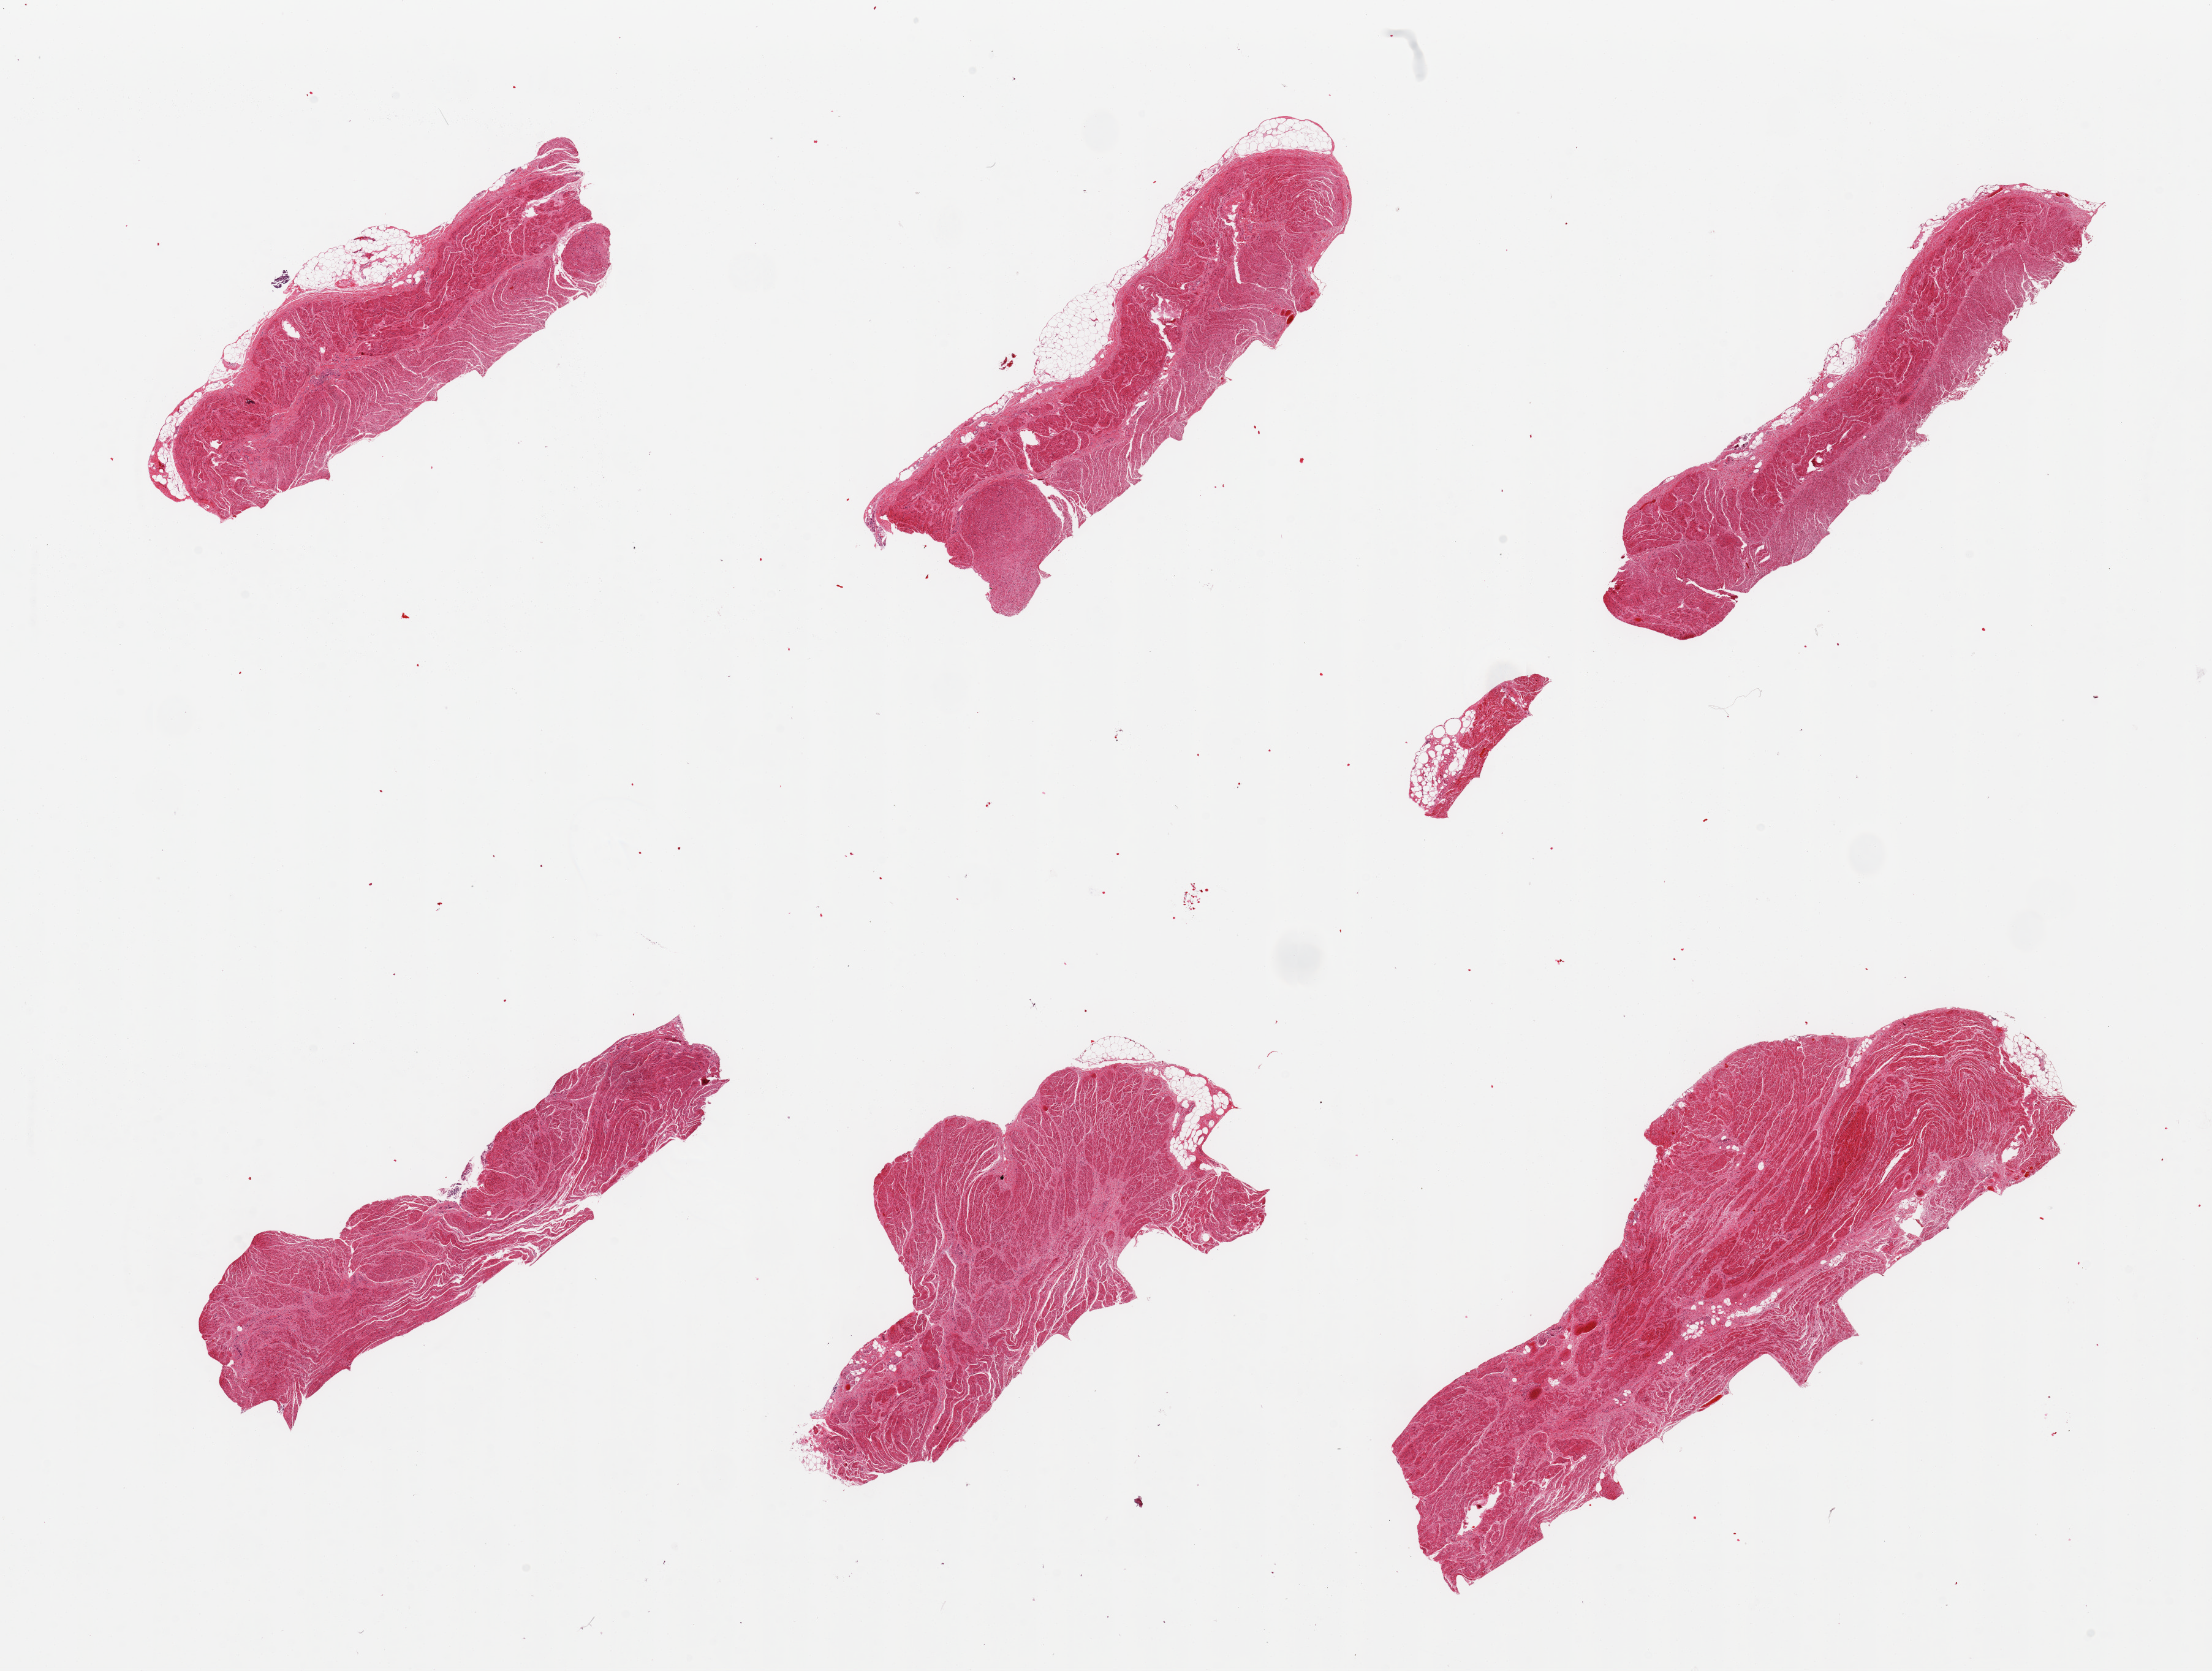
Whole-slide image, haematoxylin and eosin stain — whole scanned area (about 28.5 x 21.6 mm) shown as a low-resolution overview. PAXgene-fixed, paraffin-embedded tissue. Target tissue: gastroesophageal junction. Tissue donor sample.
Reviewer comment on this tissue sample: 6 pieces; well dissected muscle with limited amount of extraneous fat.